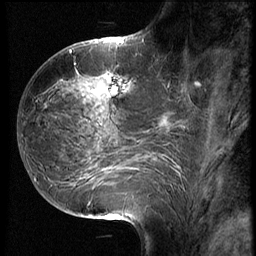
Breast MRI (dynamic contrast-enhanced), one sagittal slice. Slice 28 of 68 in the series (ordered by position). 3 images stored at this slice position (order not interpretable as contrast timing). 1.5 T. TE 4.2 ms, TR 8.9 ms. 2.5 mm slice thickness. 256 × 256 image matrix, field of view 200 × 200 mm. Patient: female, 39 years. From the clinical record (not read from this slice): setting: breast cancer imaged before/during neoadjuvant chemotherapy; receptor status: HER2-positive.
Structures marked on this image (semi-automatic segmentation, software-assisted and operator-edited):
- analysis volume of interest (the breast-tissue region the enhancement analysis was run in; not a lesion): bounding box <66,68,141,127> (left, top, right, bottom; pixels)
- tumour enhancement mask (voxels above the 140 % enhancement threshold inside the analysis volume of interest): <109,89,113,93>